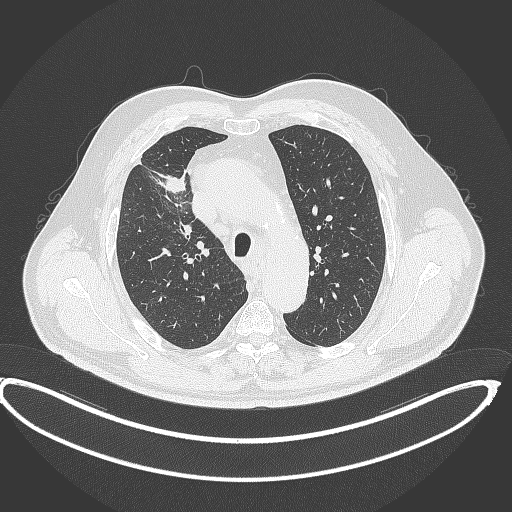
Chest CT, one axial slice; slice 300 of 390 in the series (ordered by position); lung window (W 1500 / L -600 HU); 1 mm slice thickness; 512 × 512 image matrix. Male patient, age 62 years. Case-level facts recorded for this patient, not image findings: clinical TNM (as recorded): T1c N3 M1c.
Structures marked on this image (rectangle marked by the reading radiologist):
- lung tumour (recorded histology: adenocarcinoma): bounding box [x1, y1, x2, y2] px = [157, 171, 187, 194]